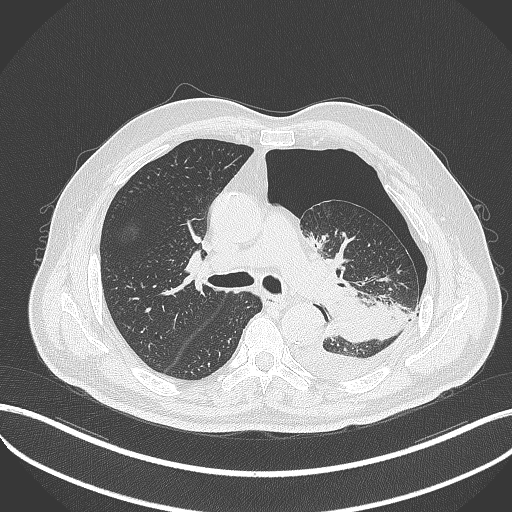
Chest CT, one axial slice. Position 323 of 464 along the scan axis. Reconstruction kernel B70f. 120 kVp. Lung window (W 1500 / L -600 HU). 1 mm slice thickness. 512 × 512 image matrix, field of view 400 × 400 mm. Male patient, age 76 years. From the clinical record (not read from this slice): clinical TNM (as recorded): T3 N0 M1b.
Outlined on this slice (bounding box drawn by a radiologist):
- lung tumour (recorded histology: adenocarcinoma): bounding box (x1, y1, x2, y2) in pixels: (319, 287, 398, 349)